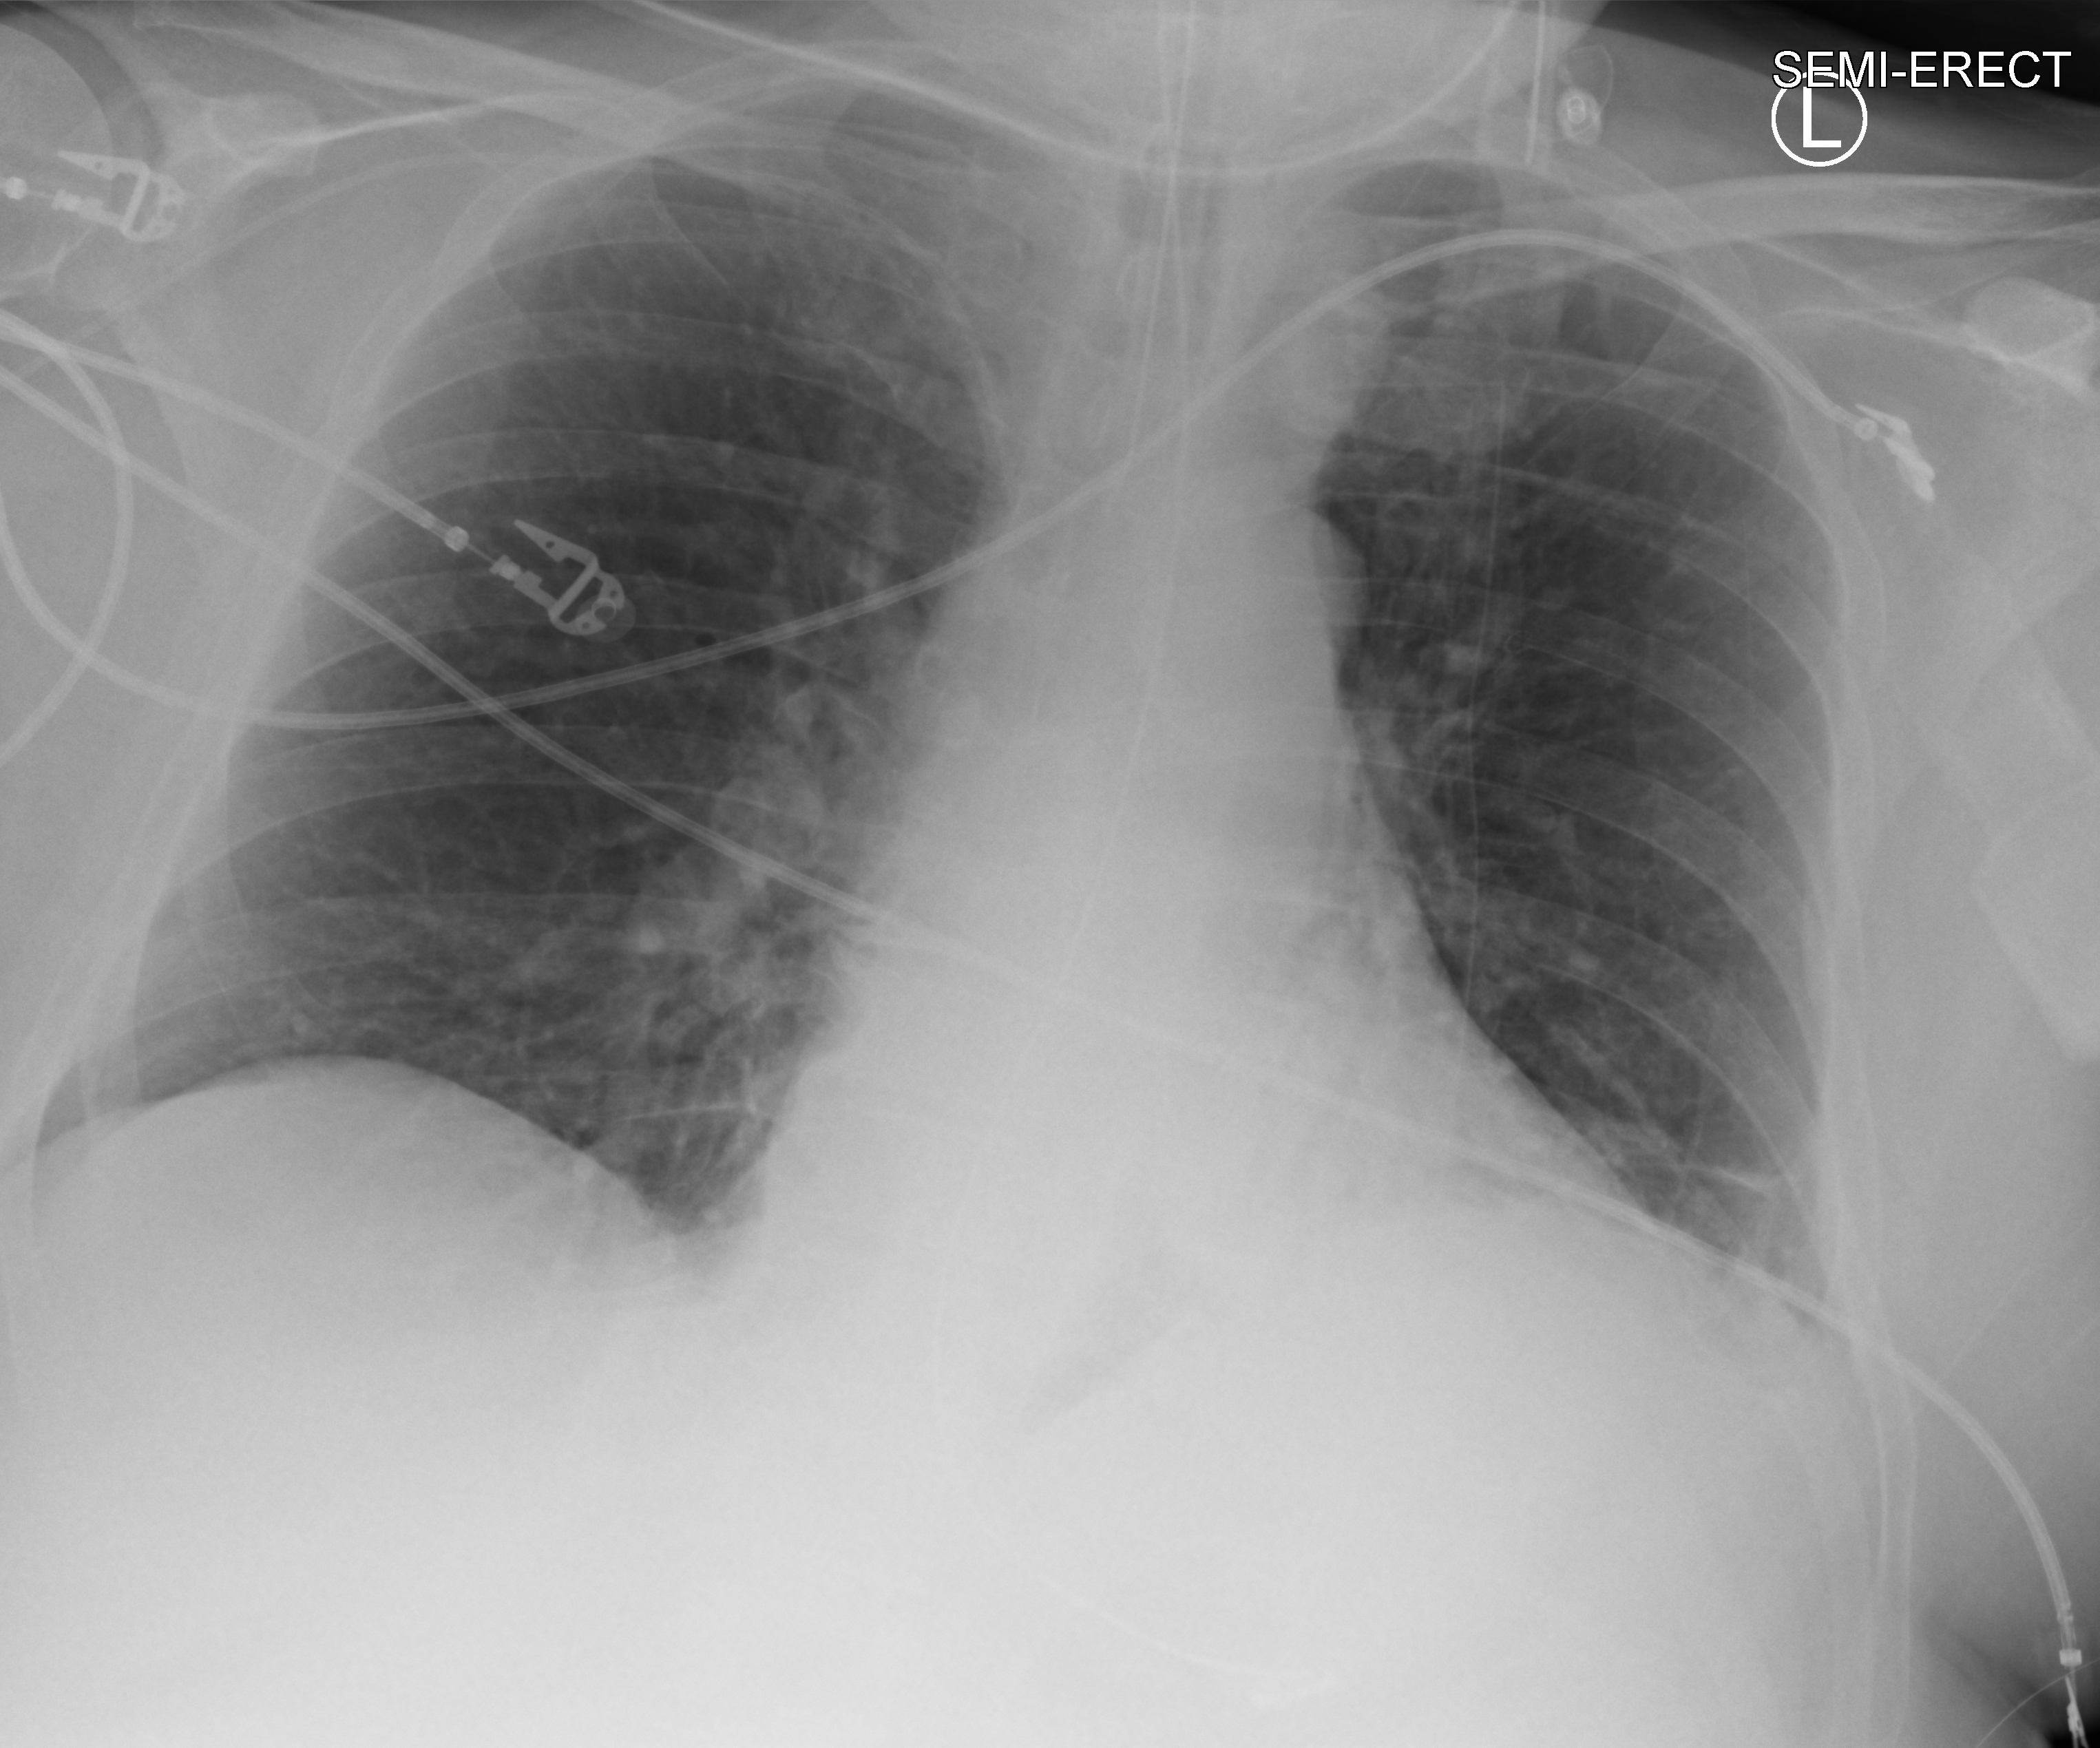
Chest X-ray (portable); anteroposterior (AP) projection. Patient hospitalised with COVID-19; male, aged 60–74 years.
Admission-level facts for this patient (not findings on this image; timing relative to this image not recorded): admitted to intensive care during this hospital stay: yes.